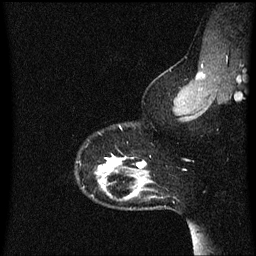
Breast MRI (dynamic contrast-enhanced), one sagittal slice; position 51 of 60 along the scan axis; dynamic contrast-enhanced series, image 2 of 3 at this slice position (ordered by acquisition); 1.5 T; TE 4.2 ms, TR 8.4 ms; 2 mm slice thickness; 256 × 256 image matrix. Patient: female, 33 years.
Outlined on this slice (semi-automatically segmented with operator editing):
- analysis volume of interest (the breast-tissue region the enhancement analysis was run in; not a lesion): box from (x=76, y=126) to (x=152, y=191) px
- tumour enhancement mask (voxels above the 70 % enhancement threshold inside the analysis volume of interest): (x=98, y=154)–(x=147, y=179)